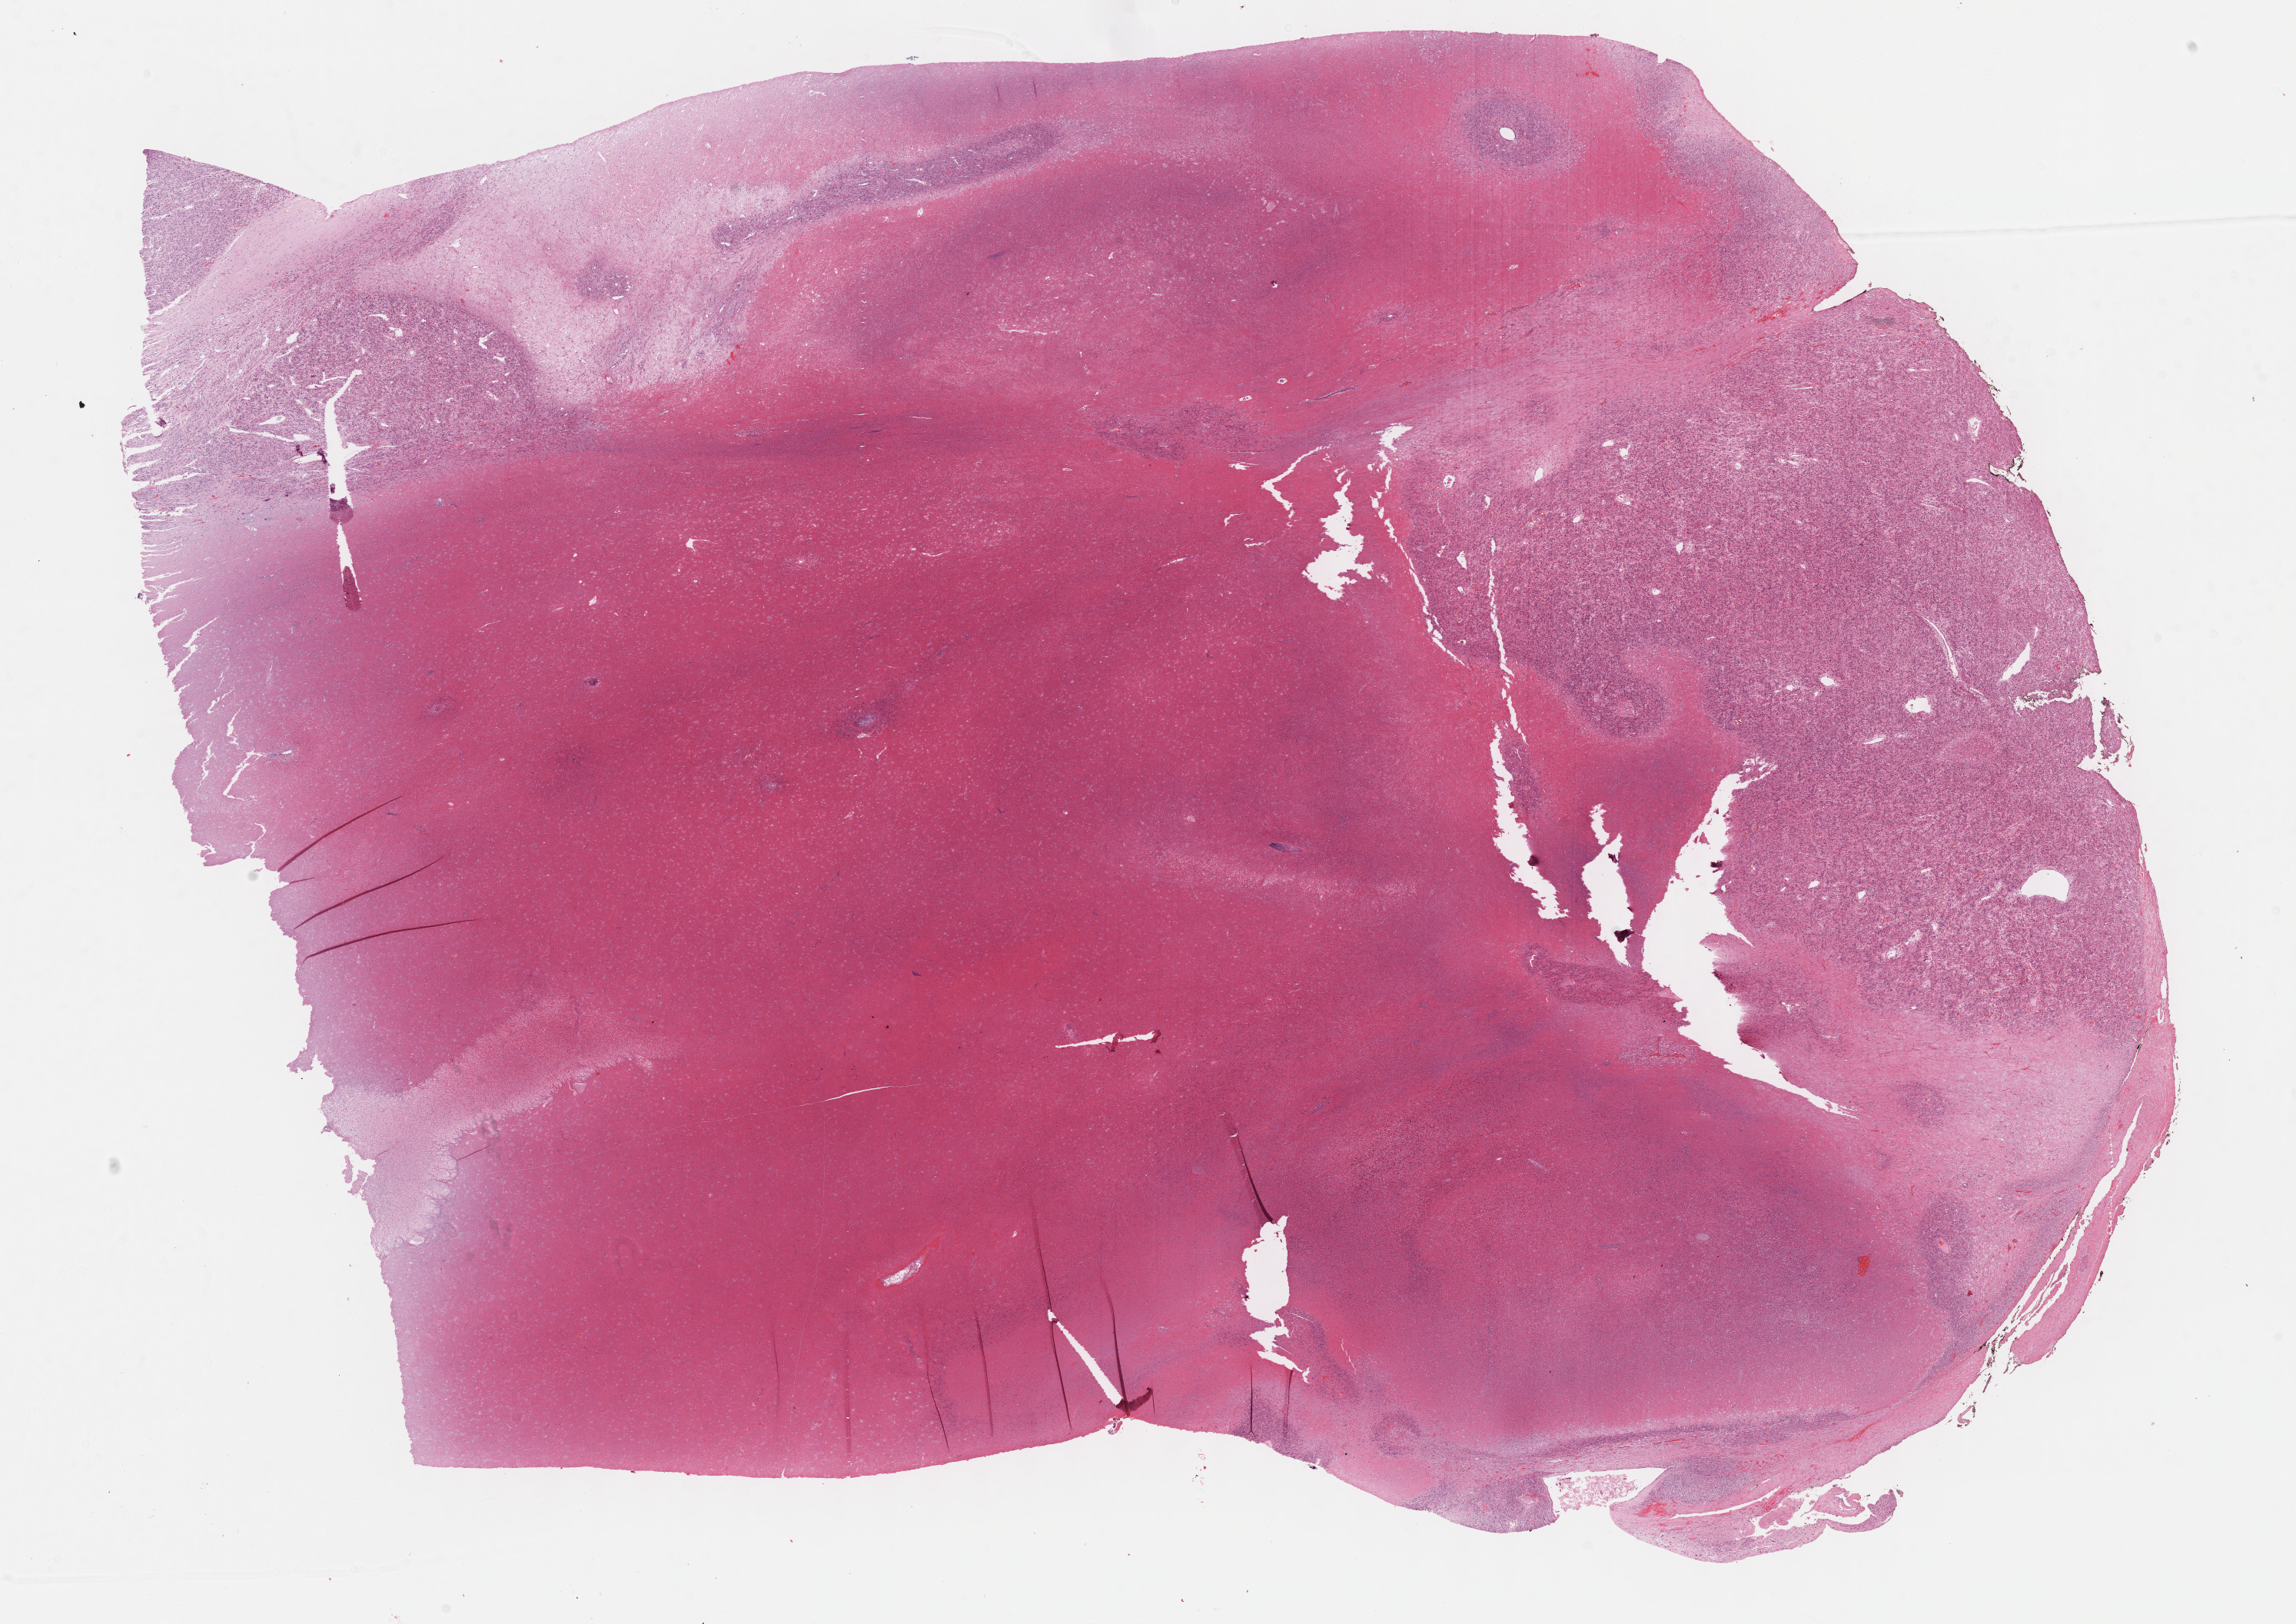
H&E-stained whole-slide image — whole scanned area (about 24.2 x 17.1 mm, slide scanned at 40x) shown as a low-resolution overview. FFPE section. Primary tumour sample from the retroperitoneum and peritoneum. Female, age 53 years at initial diagnosis.
* diagnosis: Leiomyosarcoma, NOS (retroperitoneum)